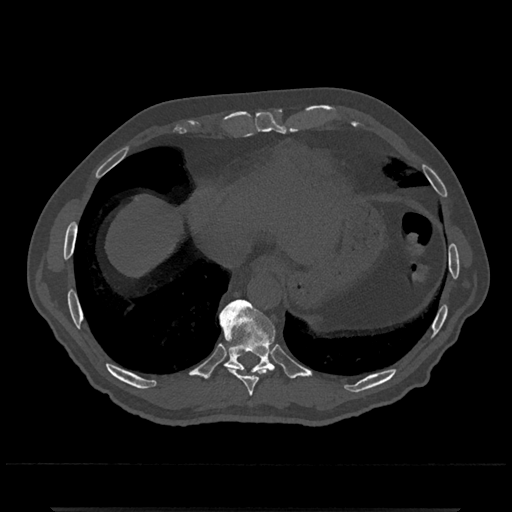
CT including the spine, one axial slice. Slice 583 of 797 in the series (ordered by position). Bone window (W 1800 / L 400 HU). 512 × 512 image matrix, field of view 393 × 393 mm. Patient: male, 67 years. From the clinical record (not read from this slice): primary cancer: prostate.
Structures marked on this image (semi-automatically segmented with operator editing):
- T10 vertebra: bounding box (x1, y1, x2, y2) in pixels: (219, 299, 276, 374)
- T9 vertebra: (227, 367, 266, 396)